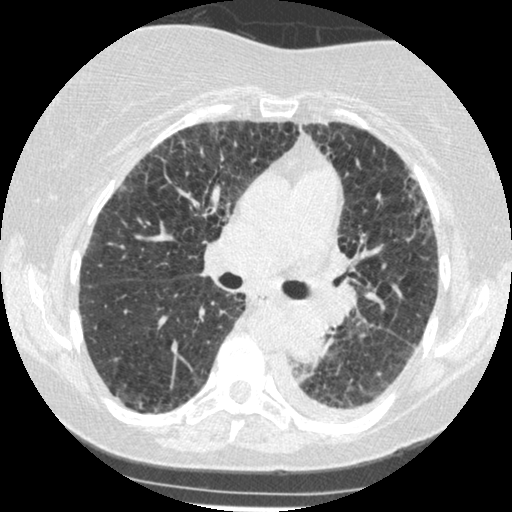
Low-dose screening chest CT, one axial slice; position 154 of 341 along the scan axis; reconstruction kernel STANDARD; 120 kVp; lung window (W 1500 / L -600 HU); 1.25 mm slice thickness; 512 × 512 image matrix, field of view 310 × 310 mm.
Structures marked on this image (manually delineated by an expert):
- lesion 1 (tumor, lower lobe of left lung): box from (x=288, y=307) to (x=329, y=363) px